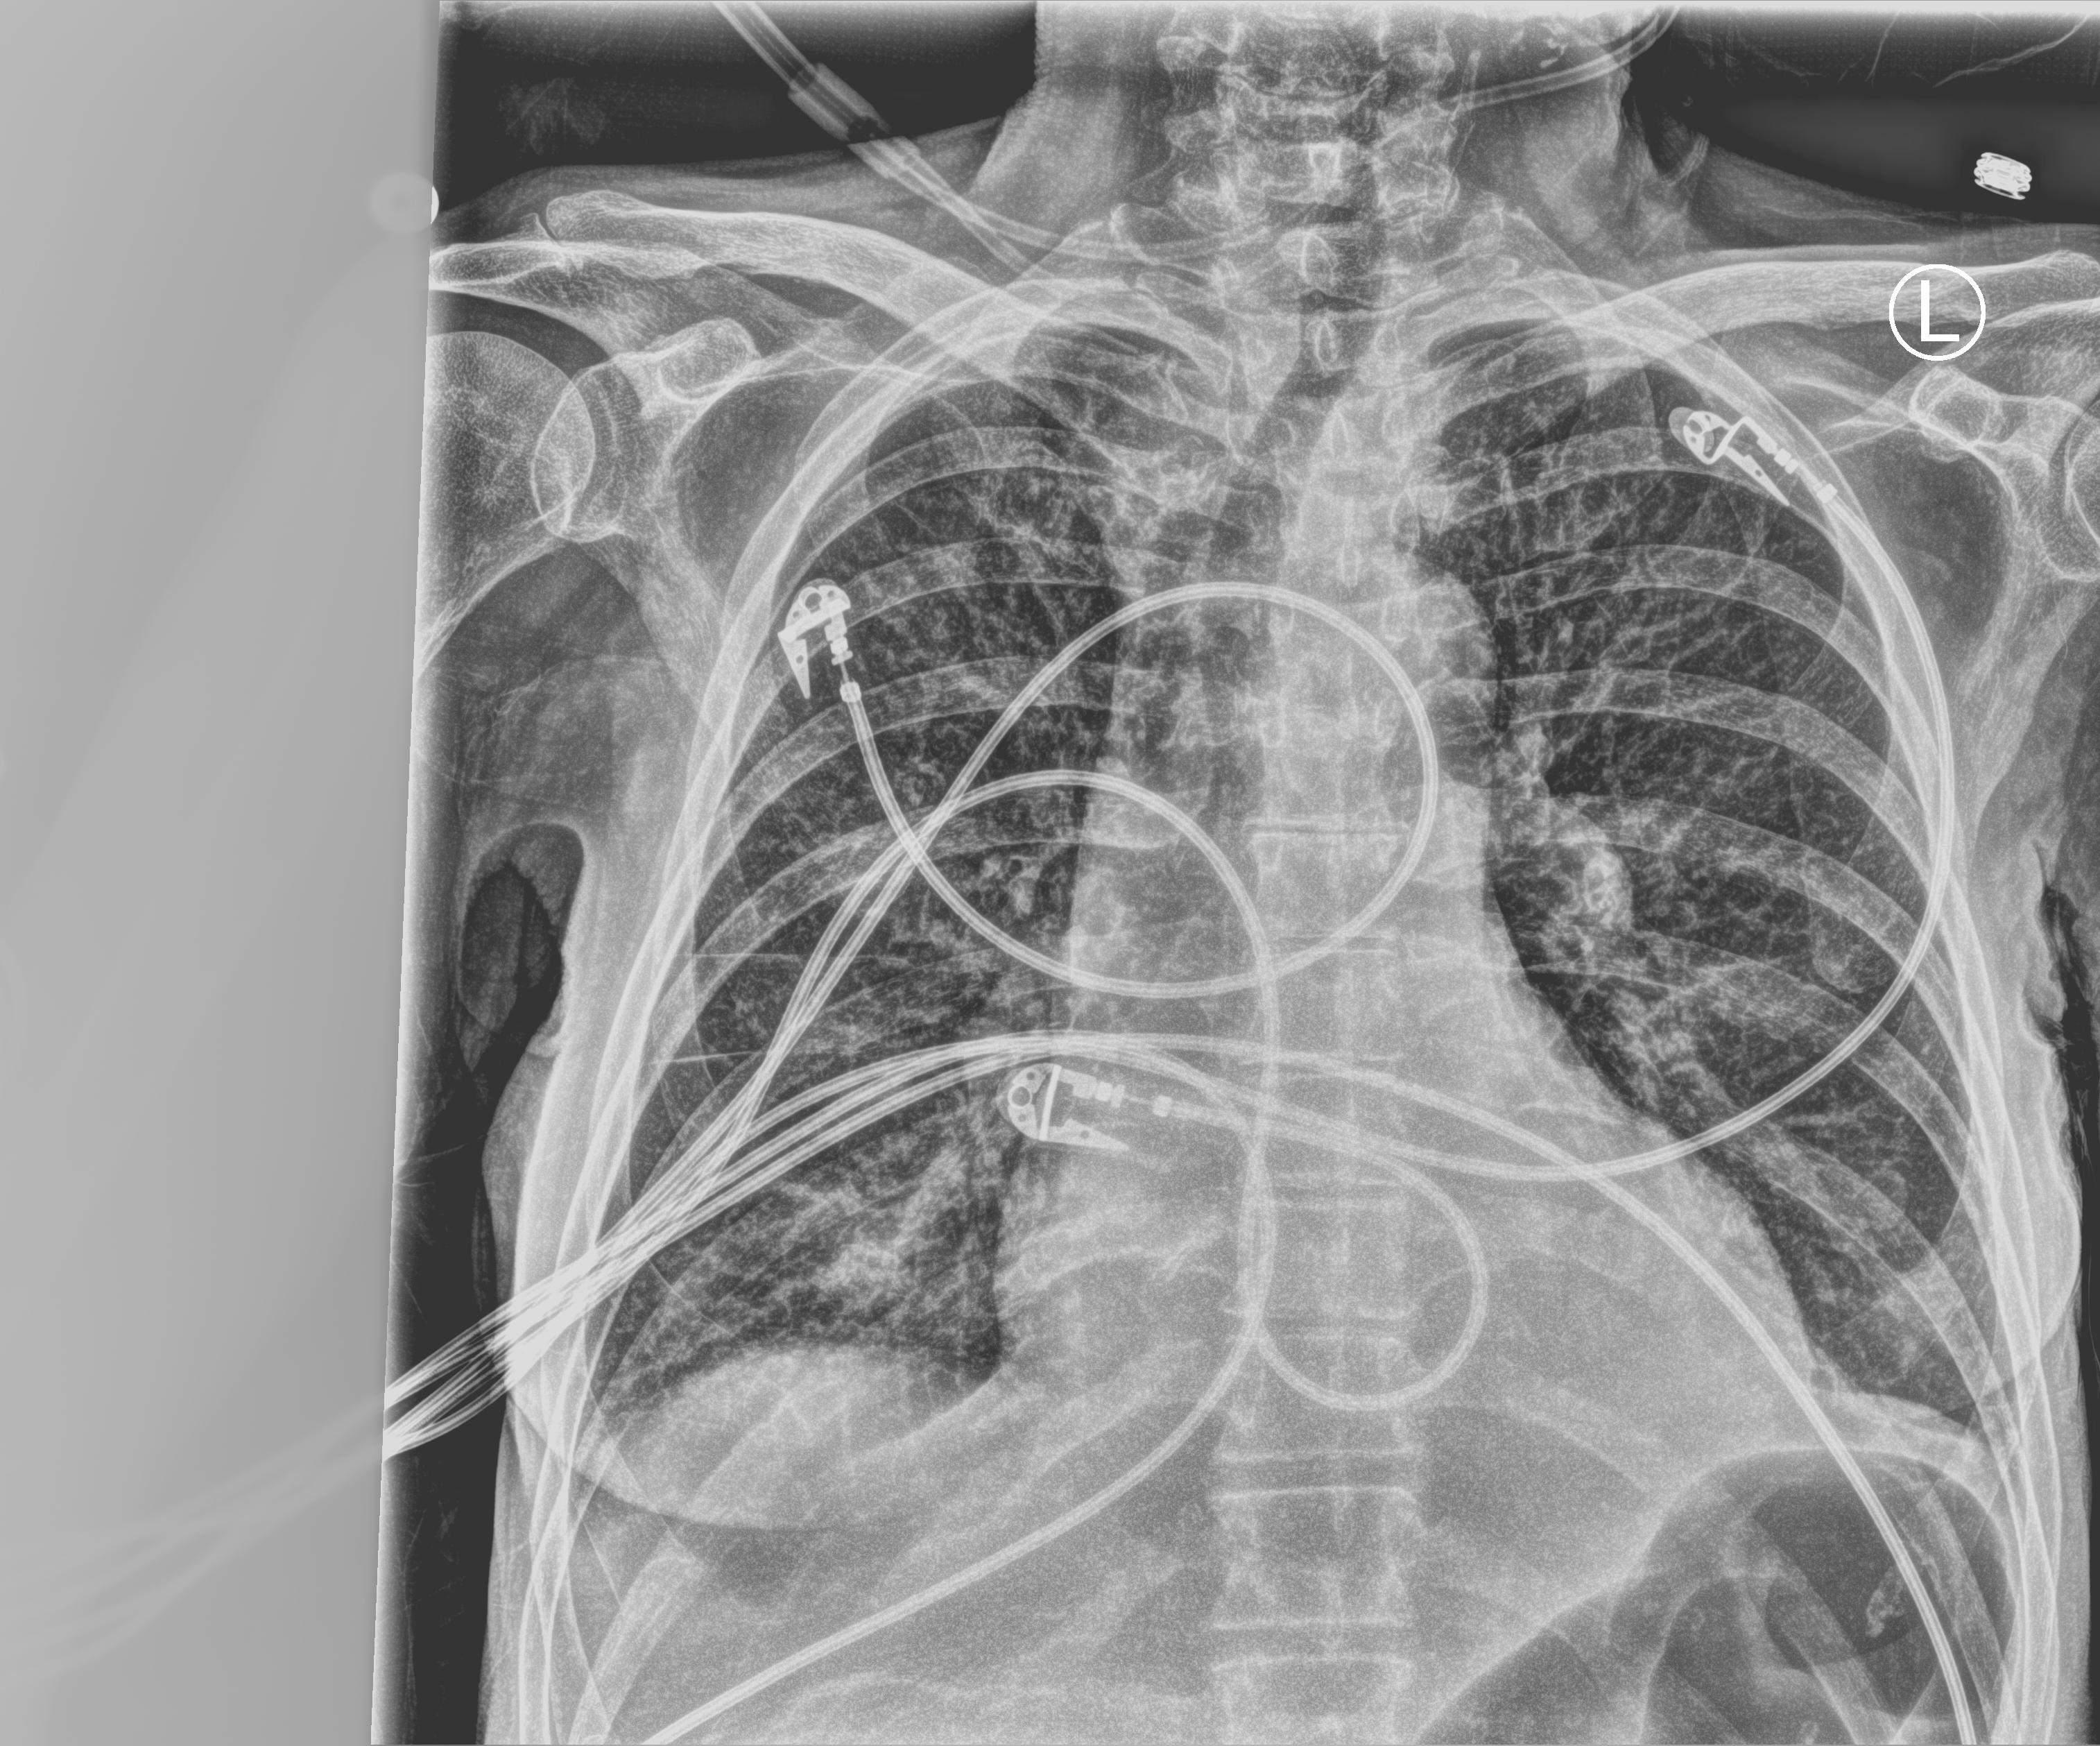
Portable chest radiograph; anteroposterior (AP) projection. Female patient hospitalised with COVID-19, age 60–74 years.
Admission-level facts for this patient (not findings on this image; timing relative to this image not recorded):
- admitted to intensive care during this hospital stay: yes